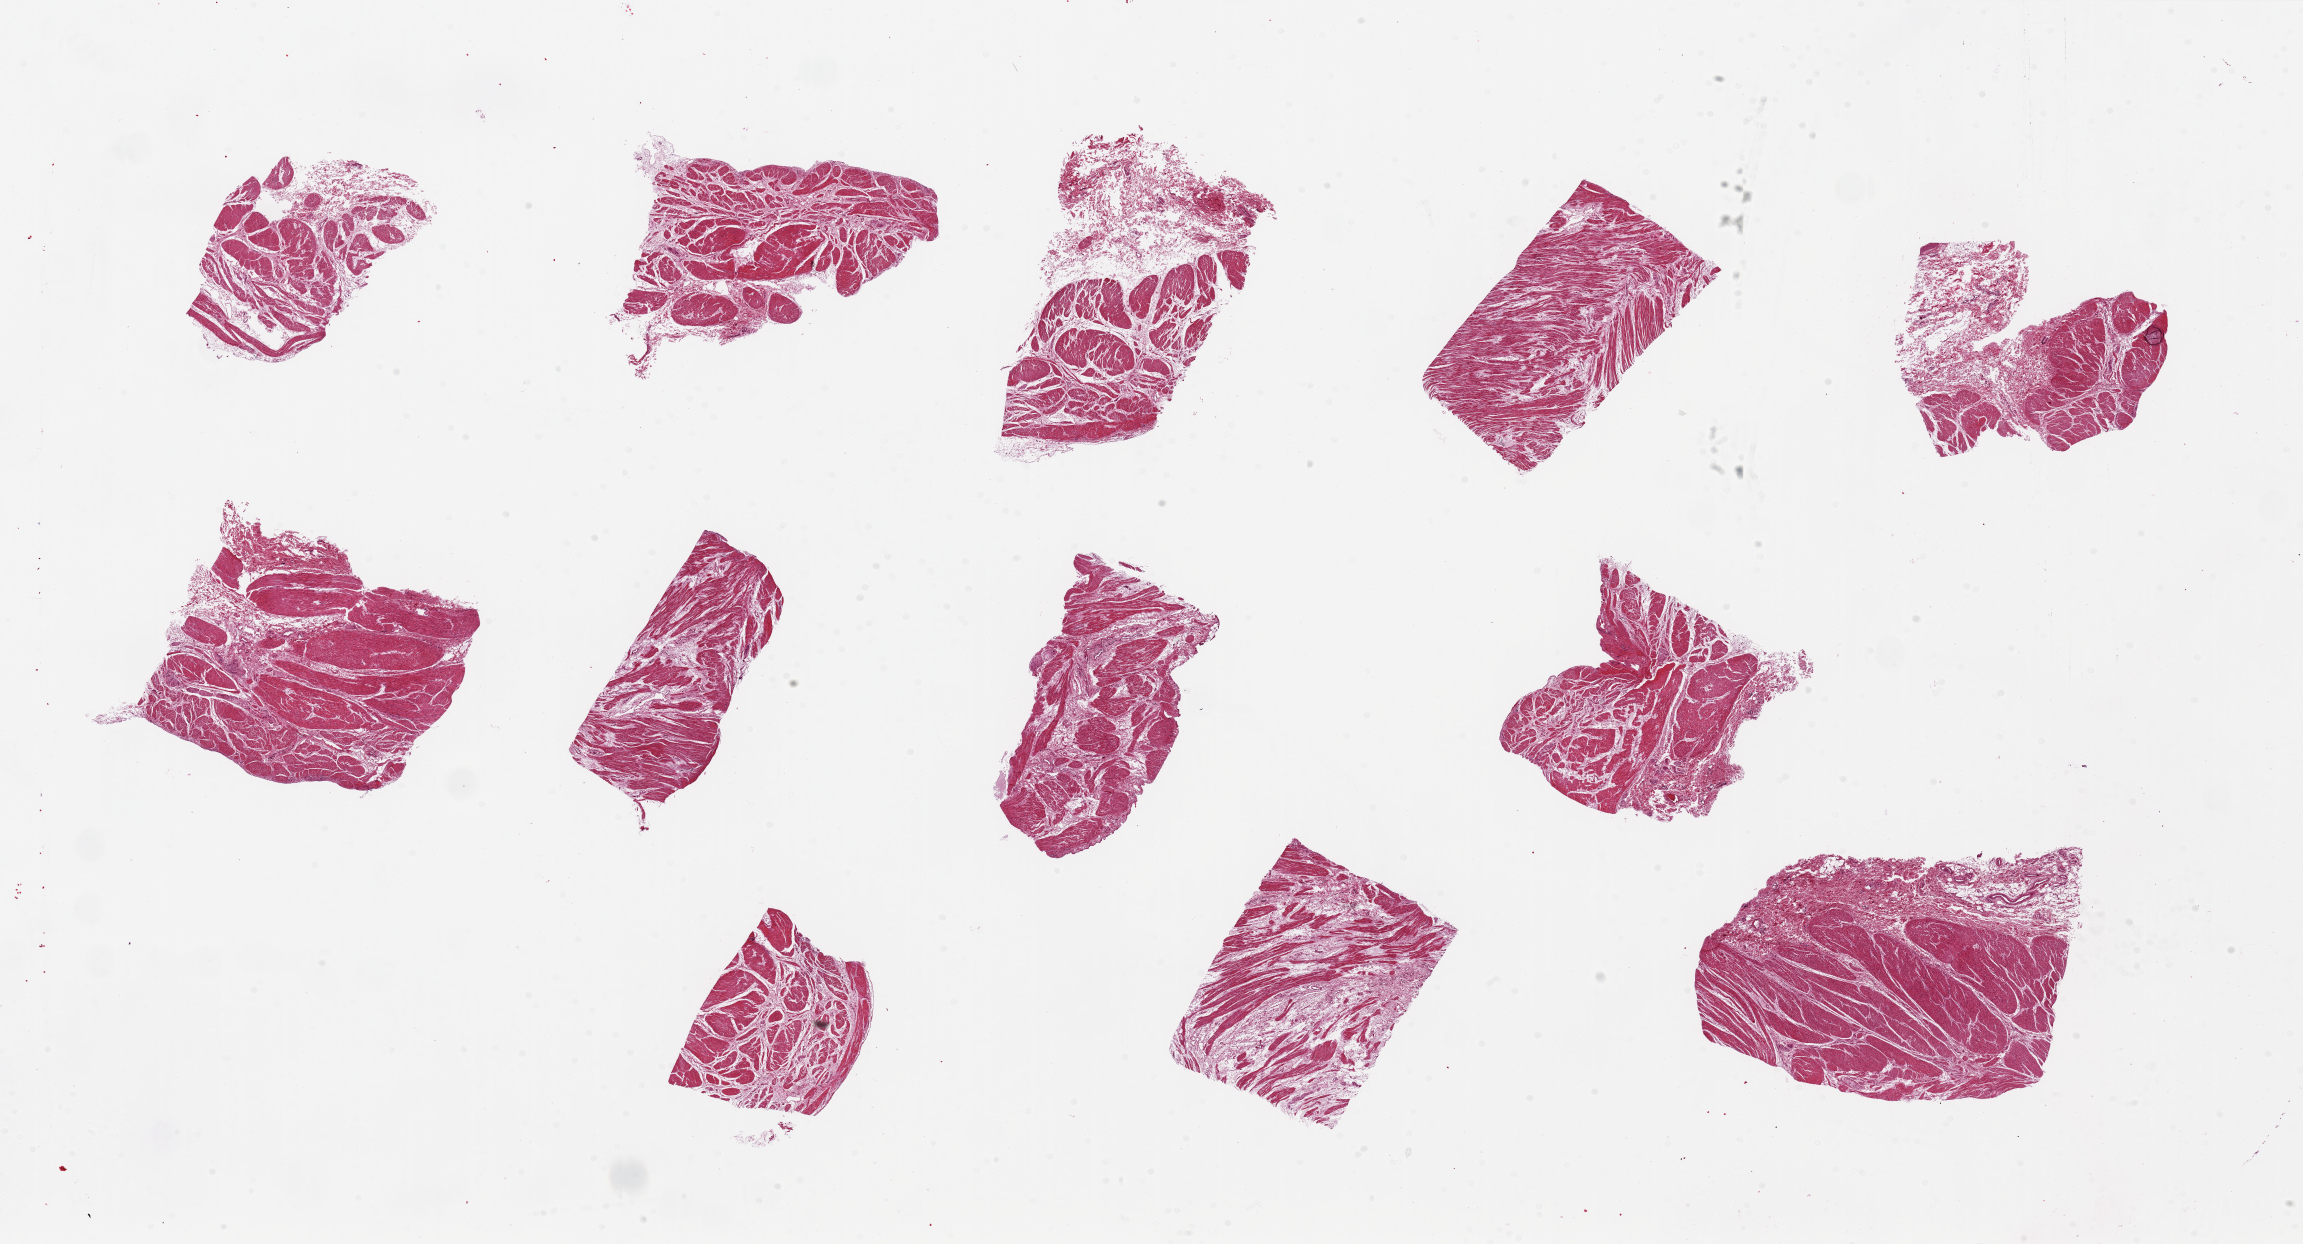
Haematoxylin and eosin whole-slide image, low-resolution overview of the scanned area, about 36.4 x 19.7 mm (acquisition: 20x scan); PAXgene-fixed, paraffin-embedded tissue; section of stomach (target tissue); tissue donor sample. Donor: male.
Review note (as recorded): 6 pieces, up to 10x5mm; all muscularis, no mucosa.